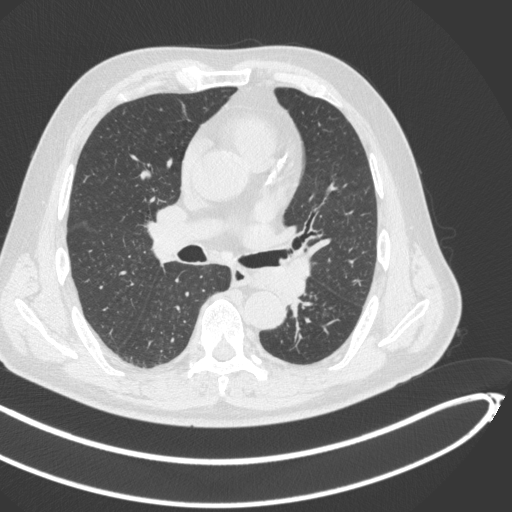
Chest CT, one axial slice; position 261 of 466 along the scan axis; 120 kVp; lung window (W 1500 / L -600 HU); 1 mm slice thickness; 512 × 512 image matrix, field of view 400 × 400 mm. Male patient, age 64 years. Case-level facts recorded for this patient, not image findings: clinical TNM (as recorded): T1c N0 M0; histopathological grade: G2.
Annotated regions visible in this slice (rectangle marked by the reading radiologist):
- lung tumour (recorded histology: squamous cell carcinoma): box from (x=248, y=252) to (x=311, y=303) px